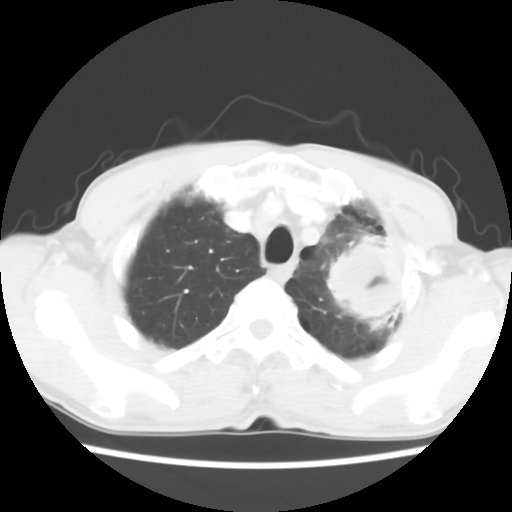
Chest CT, one axial slice. Position 50 of 60 along the scan axis. Reconstruction kernel STANDARD. 120 kVp. Lung window (W 1500 / L -600 HU). 5 mm slice thickness. 512 × 512 image matrix, field of view 308 × 308 mm. Male patient, age 64 years. Case-level facts recorded for this patient, not image findings: clinical TNM (as recorded): T3 N3 M0.
Outlined on this slice (bounding box drawn by a radiologist):
- lung tumour (recorded histology: adenocarcinoma): bounding box [x1, y1, x2, y2] px = [322, 232, 401, 328]